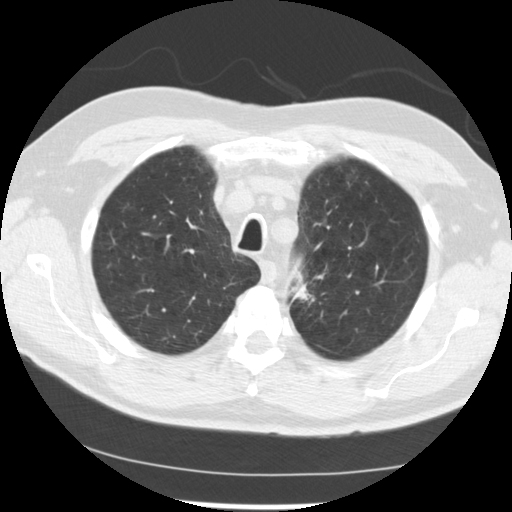
Low-dose screening chest CT, one axial slice. Slice 197 of 249 in the series (ordered by position). Reconstruction kernel STANDARD. 120 kVp. Lung window (W 1500 / L -600 HU). 2.5 mm slice thickness. 512 × 512 image matrix, field of view 341 × 341 mm.
Structures marked on this image (manually delineated by an expert):
- lesion 2 (tumor, upper lobe of left lung): bounding box (x1, y1, x2, y2) in pixels: (300, 290, 312, 300)